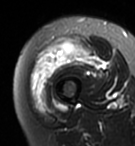
MRI of an extremity soft-tissue mass, one axial slice; slice 23 of 95 in the series (ordered by position); T2-weighted fat-saturated; MR volume resampled by the dataset authors to the PET/CT grid (not the native acquisition matrix); 3.27 mm slice thickness; 135 × 146 image matrix, field of view 132 × 143 mm. Female patient. From the clinical record (not read from this slice): histological type: pleiomorphic undifferentiated sarcoma; grade: high; site of the primary tumour: right quadricep.
Structures marked on this image (expert contour drawn on MRI and transferred to this co-registered scan by the dataset authors):
- gross tumour volume including surrounding oedema: bounding box <30,38,93,110> (left, top, right, bottom; pixels)